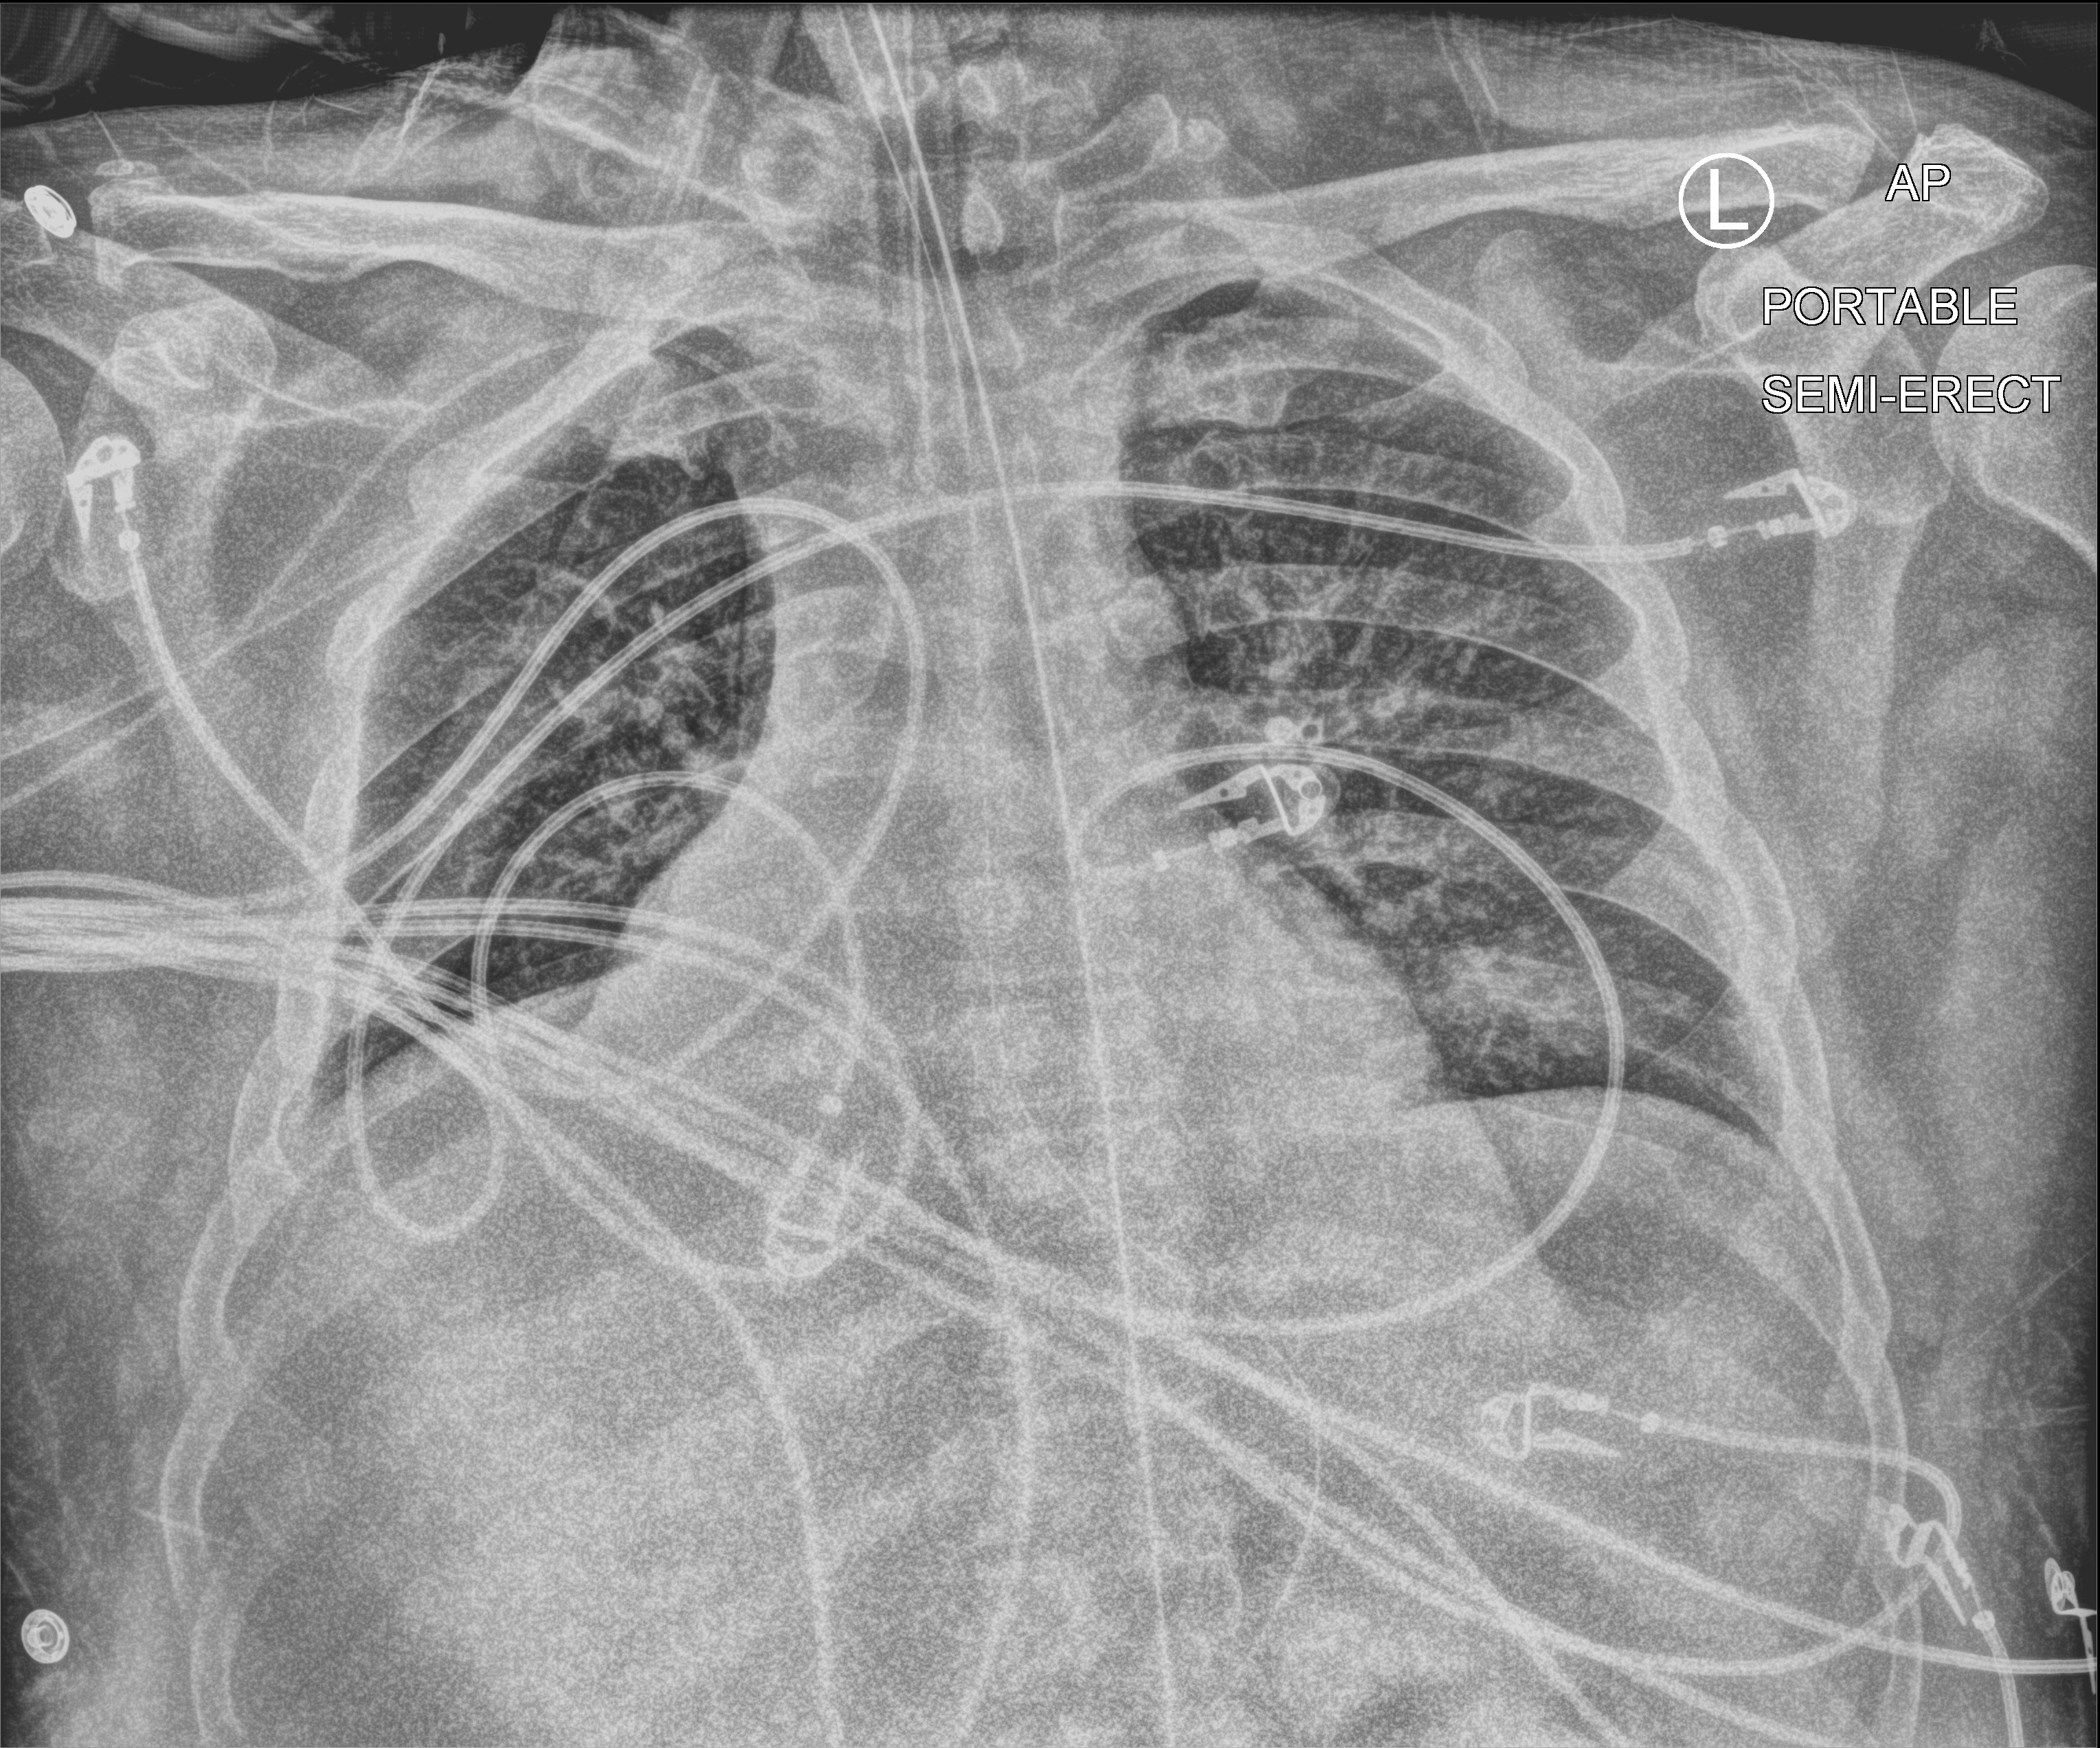
Bedside chest radiograph (computed radiography). Male patient hospitalised with COVID-19, age 18–59 years.
From the hospital-stay record, not from the radiograph (when in the stay this image was taken is not recorded): admitted to intensive care during this hospital stay: yes.